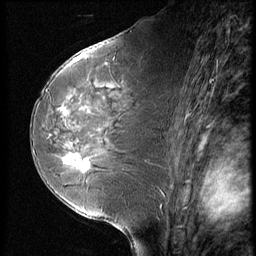
Breast MRI (dynamic contrast-enhanced), one sagittal slice. Position 34 of 56 along the scan axis. Dynamic contrast-enhanced series, image 2 of 3 at this slice position (ordered by acquisition). 1.5 T. TE 4.2 ms, TR 9 ms. 2.5 mm slice thickness. 256 × 256 image matrix. Patient: female, 58 years. From the clinical record (not read from this slice): setting: breast cancer imaged before/during neoadjuvant chemotherapy; receptor status: HR-positive, HER2-negative.
Annotated regions visible in this slice (semi-automatically segmented with operator editing):
- analysis volume of interest (the breast-tissue region the enhancement analysis was run in; not a lesion): bounding box [x1, y1, x2, y2] px = [56, 146, 99, 182]
- tumour enhancement mask (voxels above the 140 % enhancement threshold inside the analysis volume of interest): [63, 153, 90, 171]